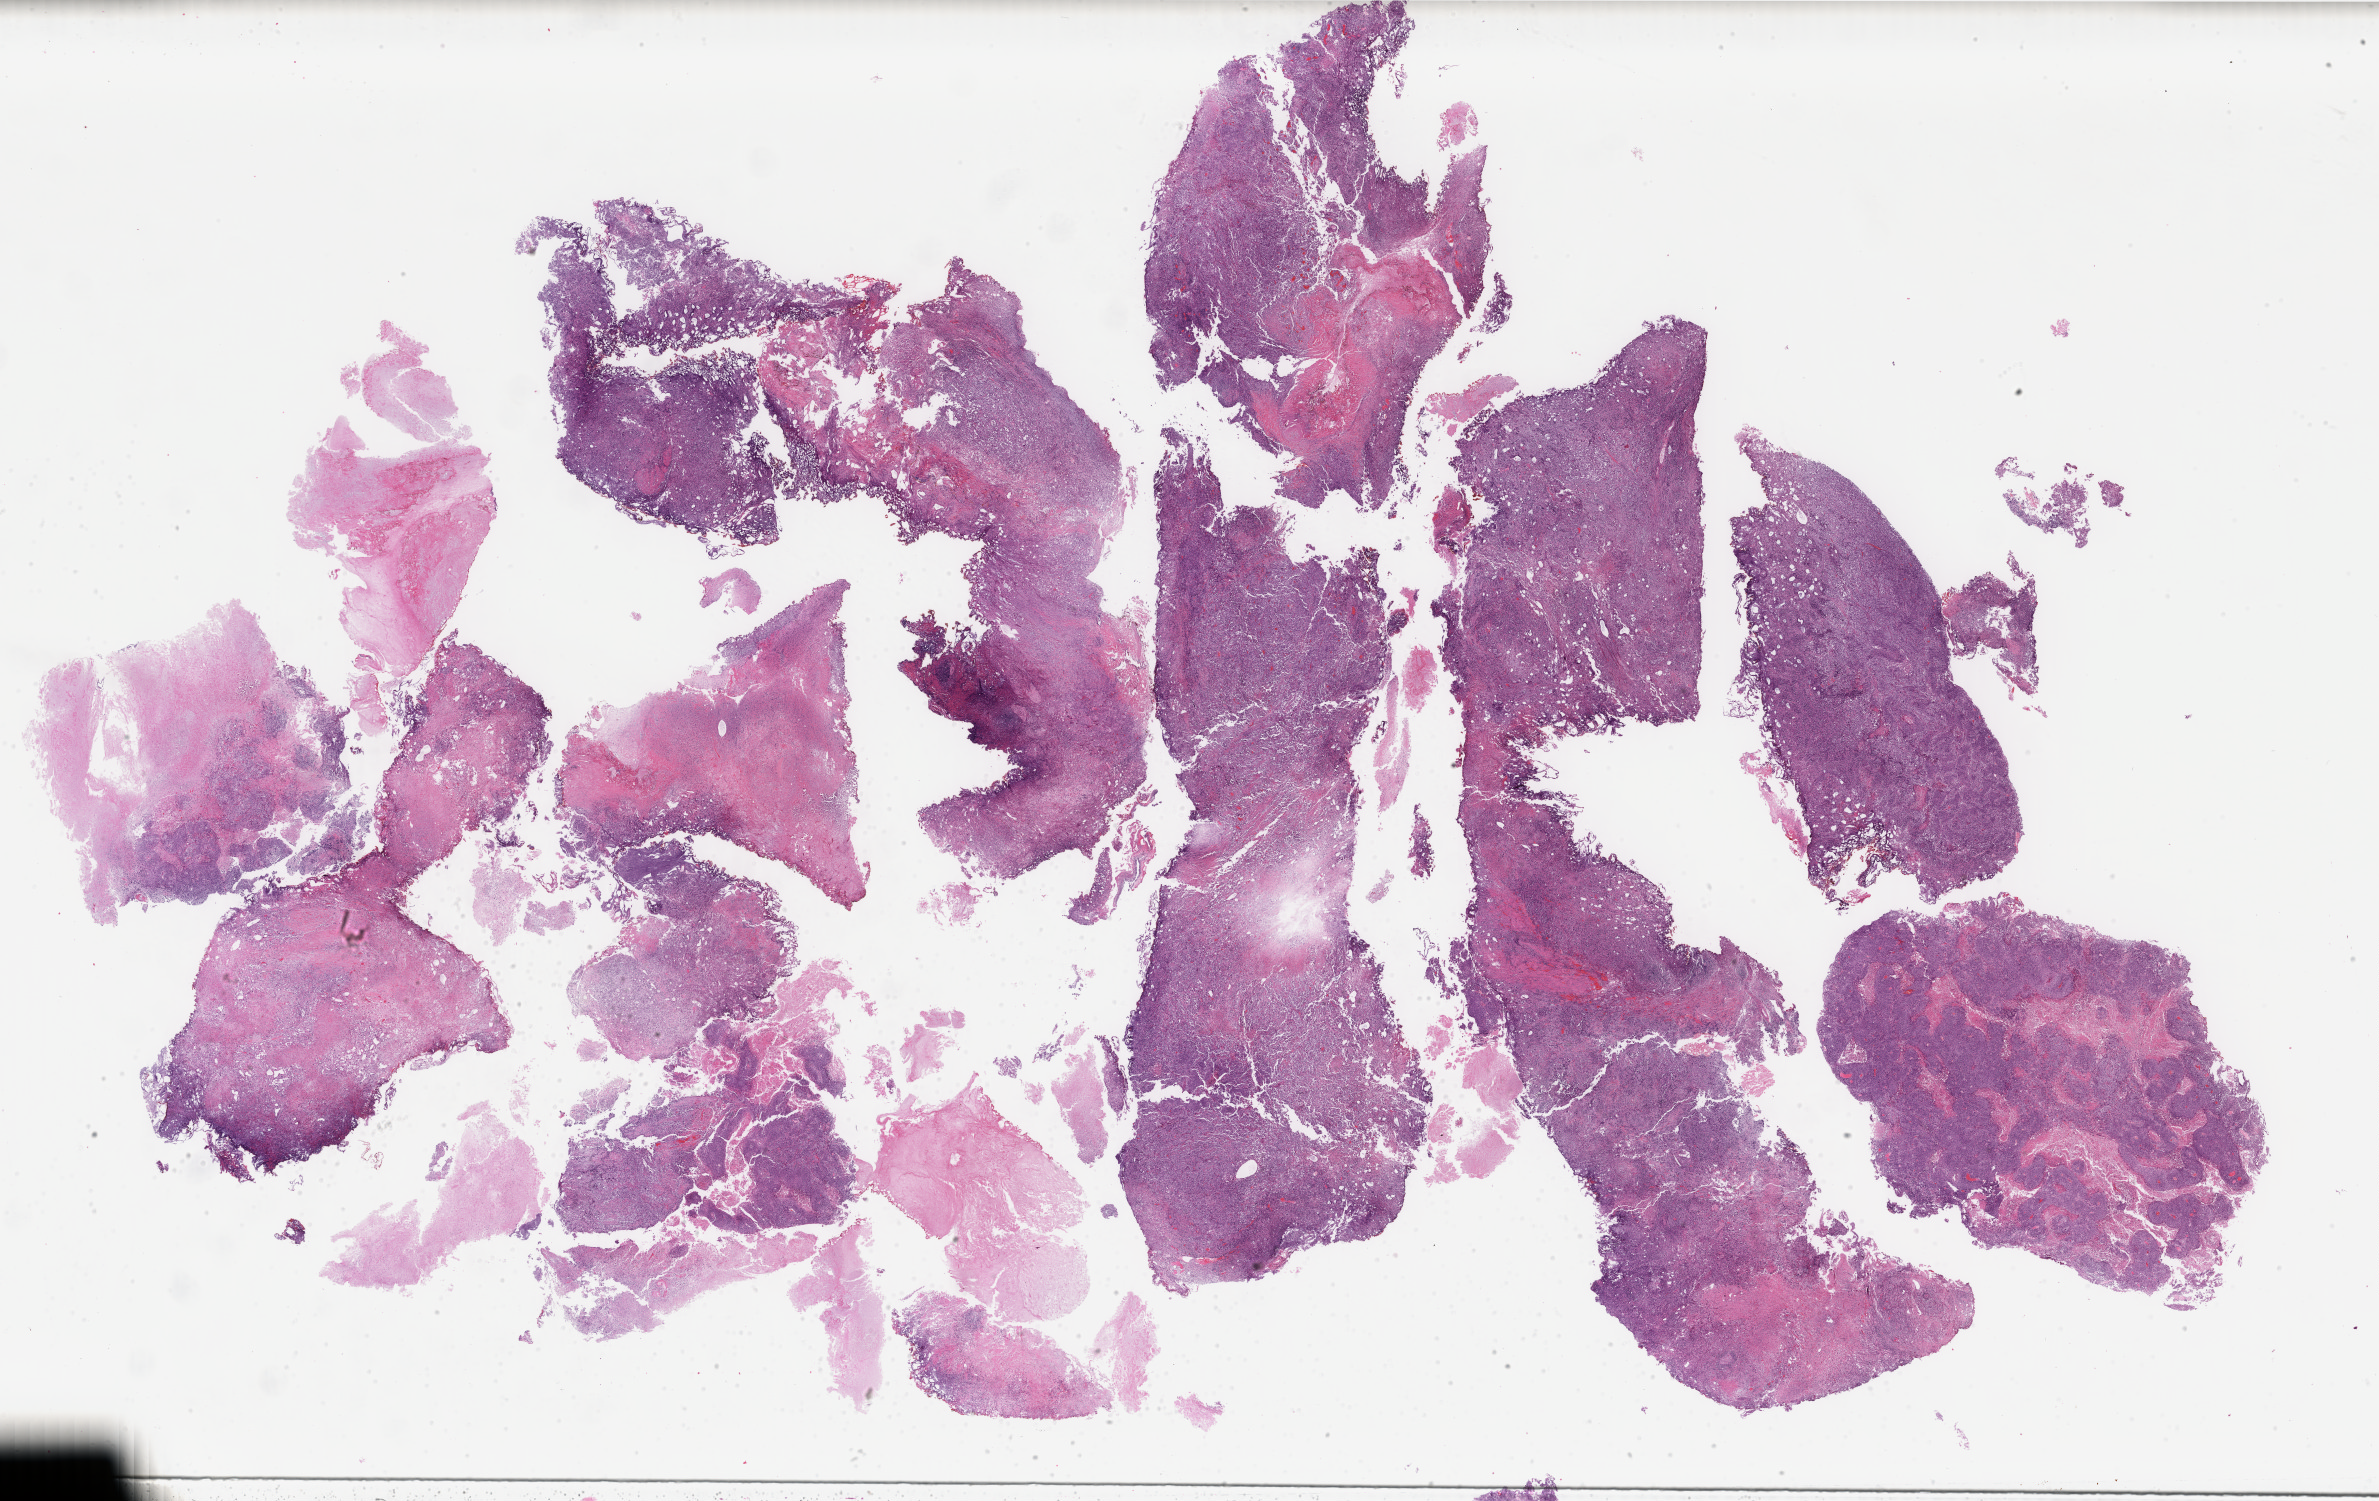
Whole-slide histology image, H&E-stained, a low-resolution overview of the entire scanned area, about 37.8 x 23.8 mm (acquisition: 40x scan), formalin-fixed paraffin-embedded (FFPE) diagnostic section, bladder, primary tumour sample. Patient: male, age at initial diagnosis 50 years.
Pathologic diagnosis: Transitional cell carcinoma.